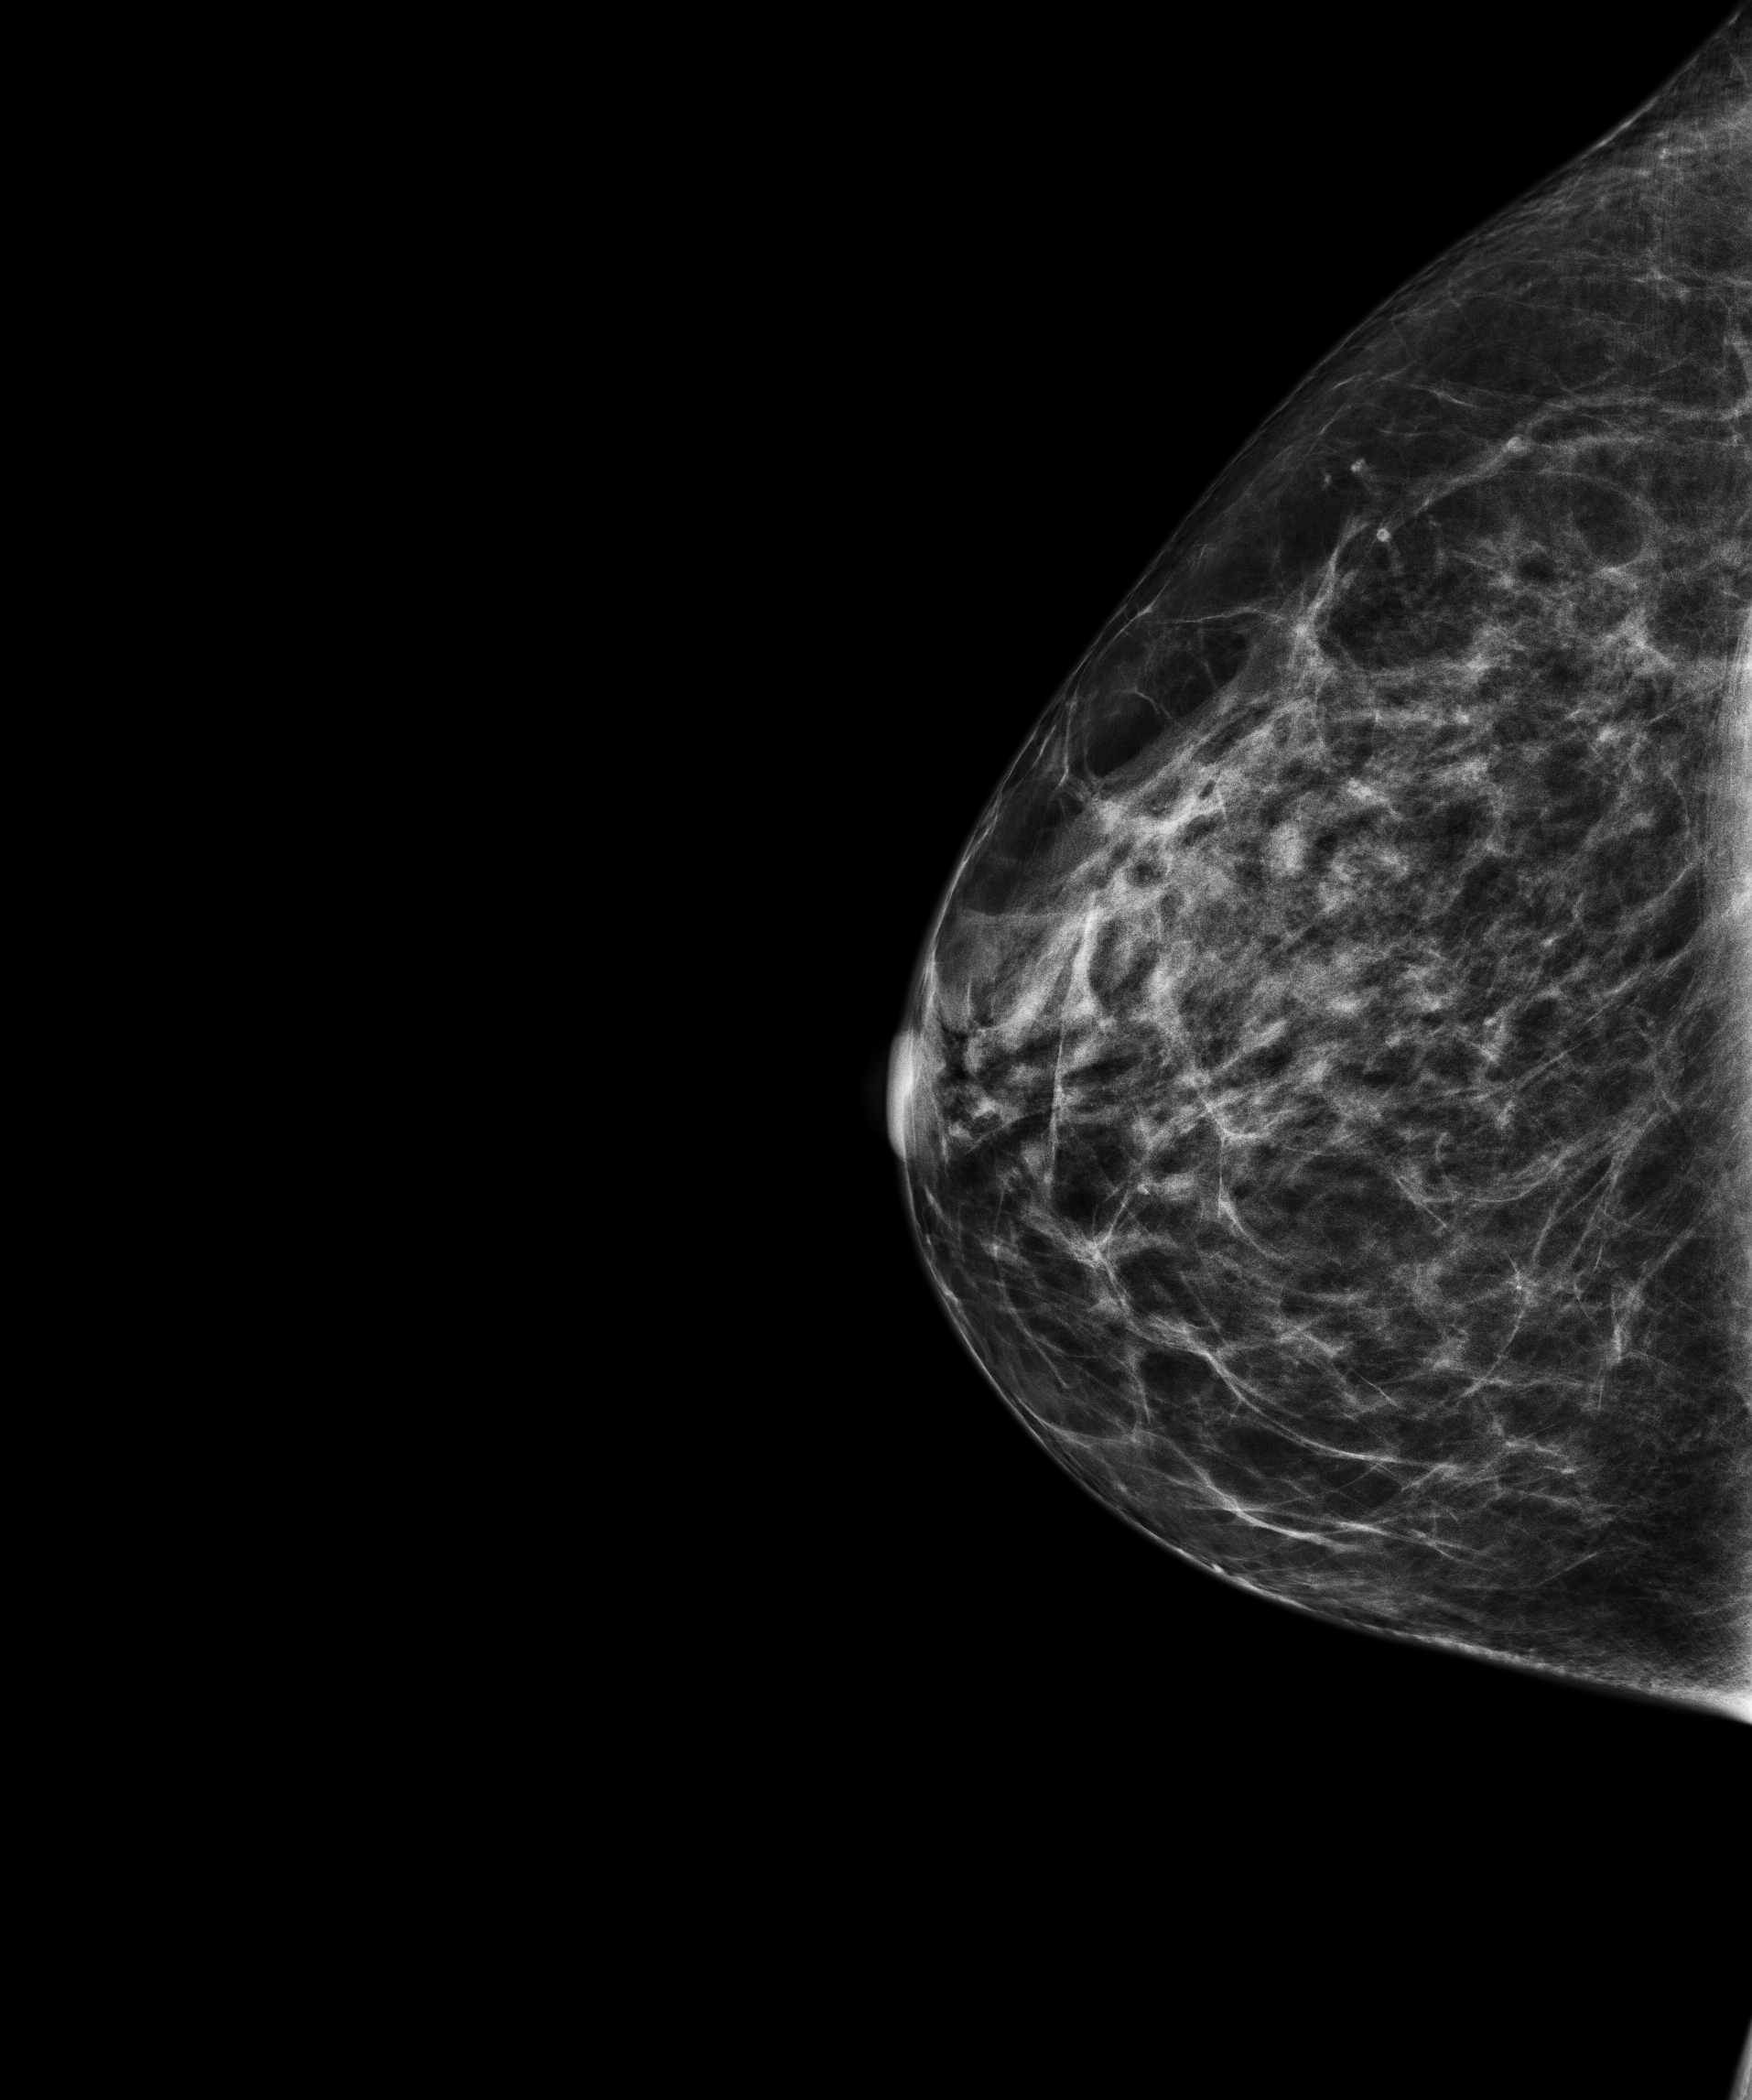
Screening examination, compressed breast thickness 61.8 mm. Patient aged 57 years (female).
Image type: full-field digital mammogram. Breast: right. Projection: craniocaudal (CC) view.